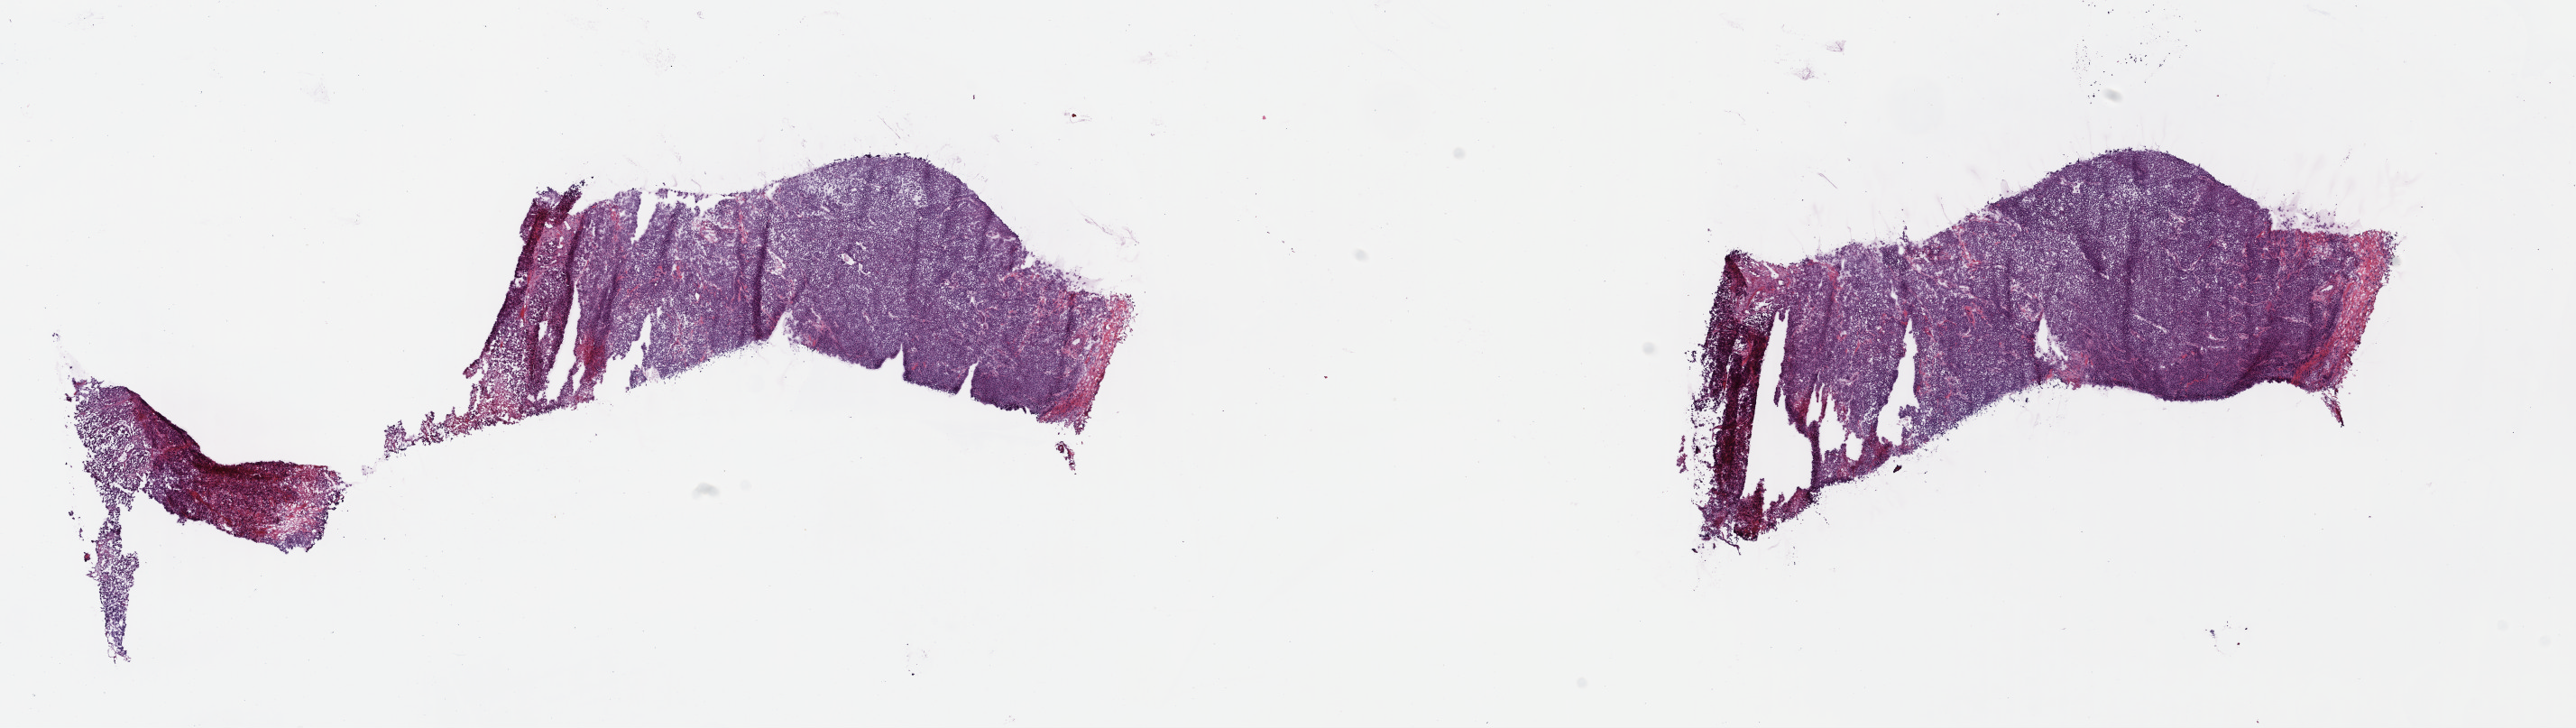
Whole-slide histology image, H&E — whole scanned area (about 22.4 x 6.3 mm, acquisition: 40x scan) shown as a low-resolution overview; frozen section; metastatic tumour sample. Patient: male, age at initial diagnosis 39 years. Composition of this section per pathologist review: tumour cells 100%, tumour nuclei 95%, normal cells 0%, stromal cells 0%, necrosis 0%. Inflammatory infiltration, as recorded: lymphocyte infiltration 0%, monocyte infiltration 0%, neutrophil infiltration 0%.
This section: metastatic tumour tissue. Patient diagnosis: Malignant melanoma, NOS.